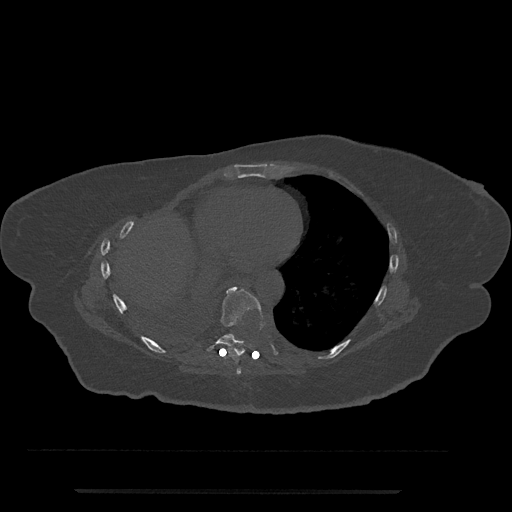
CT including the spine, one axial slice; slice 385 of 797 in the series (ordered by position); bone window (W 1800 / L 400 HU); 0.5 mm slice thickness; 512 × 512 image matrix, field of view 440 × 440 mm. Female patient, age 51 years. From the clinical record (not read from this slice): primary cancer: neuro.
Outlined on this slice (semi-automatic segmentation, software-assisted and operator-edited):
- T7 vertebra: bounding box [x1, y1, x2, y2] px = [236, 367, 241, 375]
- T8 vertebra: [207, 286, 264, 357]
- T9 vertebra: [228, 333, 235, 339]